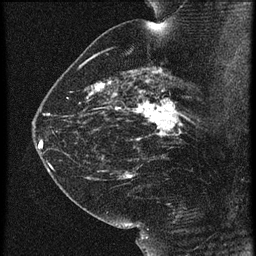
Breast MRI (dynamic contrast-enhanced), one sagittal slice; position 38 of 60 along the scan axis; 3 images stored at this slice position (order not interpretable as contrast timing); 1.5 T; TE 4.2 ms, TR 21.3 ms; 256 × 256 image matrix, field of view 180 × 180 mm. Female patient, age 42 years. Case-level facts recorded for this patient, not image findings: setting: breast cancer imaged before/during neoadjuvant chemotherapy; receptor status: HER2-positive.
Outlined on this slice (semi-automatically segmented with operator editing):
- analysis volume of interest (the breast-tissue region the enhancement analysis was run in; not a lesion): bounding box <122,82,195,147> (left, top, right, bottom; pixels)
- tumour enhancement mask (voxels above the 90 % enhancement threshold inside the analysis volume of interest): <131,82,186,141>